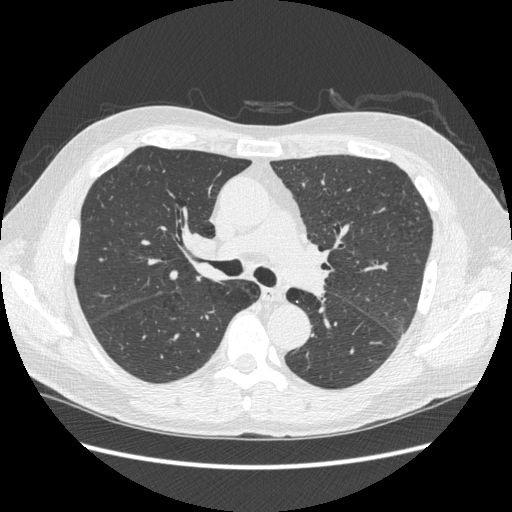
Axial slice from a low-dose chest CT screening exam, third annual screen, lung window (W 1500 / L -600 HU), 1.25 mm slice thickness, slice 105 of 258 in the series, 512 × 512 image matrix. Male, age 59 years at enrolment. Current smoker at enrolment.
Expert reader's lesion annotation, bounding box [x1, y1, x2, y2] px = [178, 225, 228, 268]. The screening reader recorded 2 non-calcified nodules or masses ≥4 mm on this exam; which of them this box marks is not recorded. Later outcome: lung cancer diagnosed 169 days after this screen — squamous cell carcinoma, keratinizing, NOS, right hilum, stage IIIB (AJCC 6th edition).